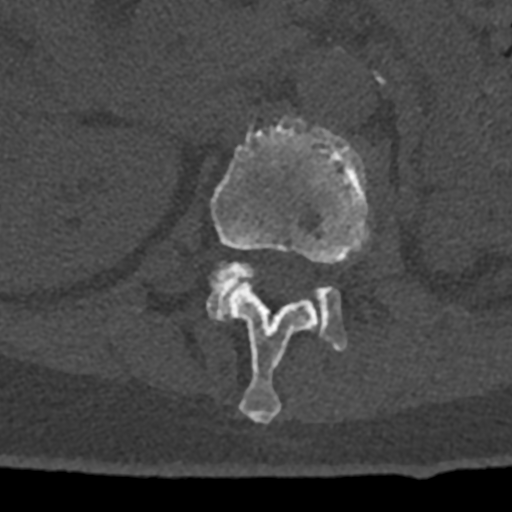
CT including the spine, one axial slice; slice 416 of 797 in the series (ordered by position); reconstruction kernel Br40s/3; 120 kVp; bone window (W 1800 / L 400 HU); 512 × 512 image matrix. Patient: male, 74 years. From the clinical record (not read from this slice): primary cancer: renal; vertebrae with lytic lesions (as recorded): T10, L1, L2, L3, L4, L5.
Structures marked on this image (semi-automatic segmentation, software-assisted and operator-edited):
- L1 vertebra: box from (x=210, y=116) to (x=370, y=424) px
- L2 vertebra: (x=206, y=261)–(x=347, y=352)